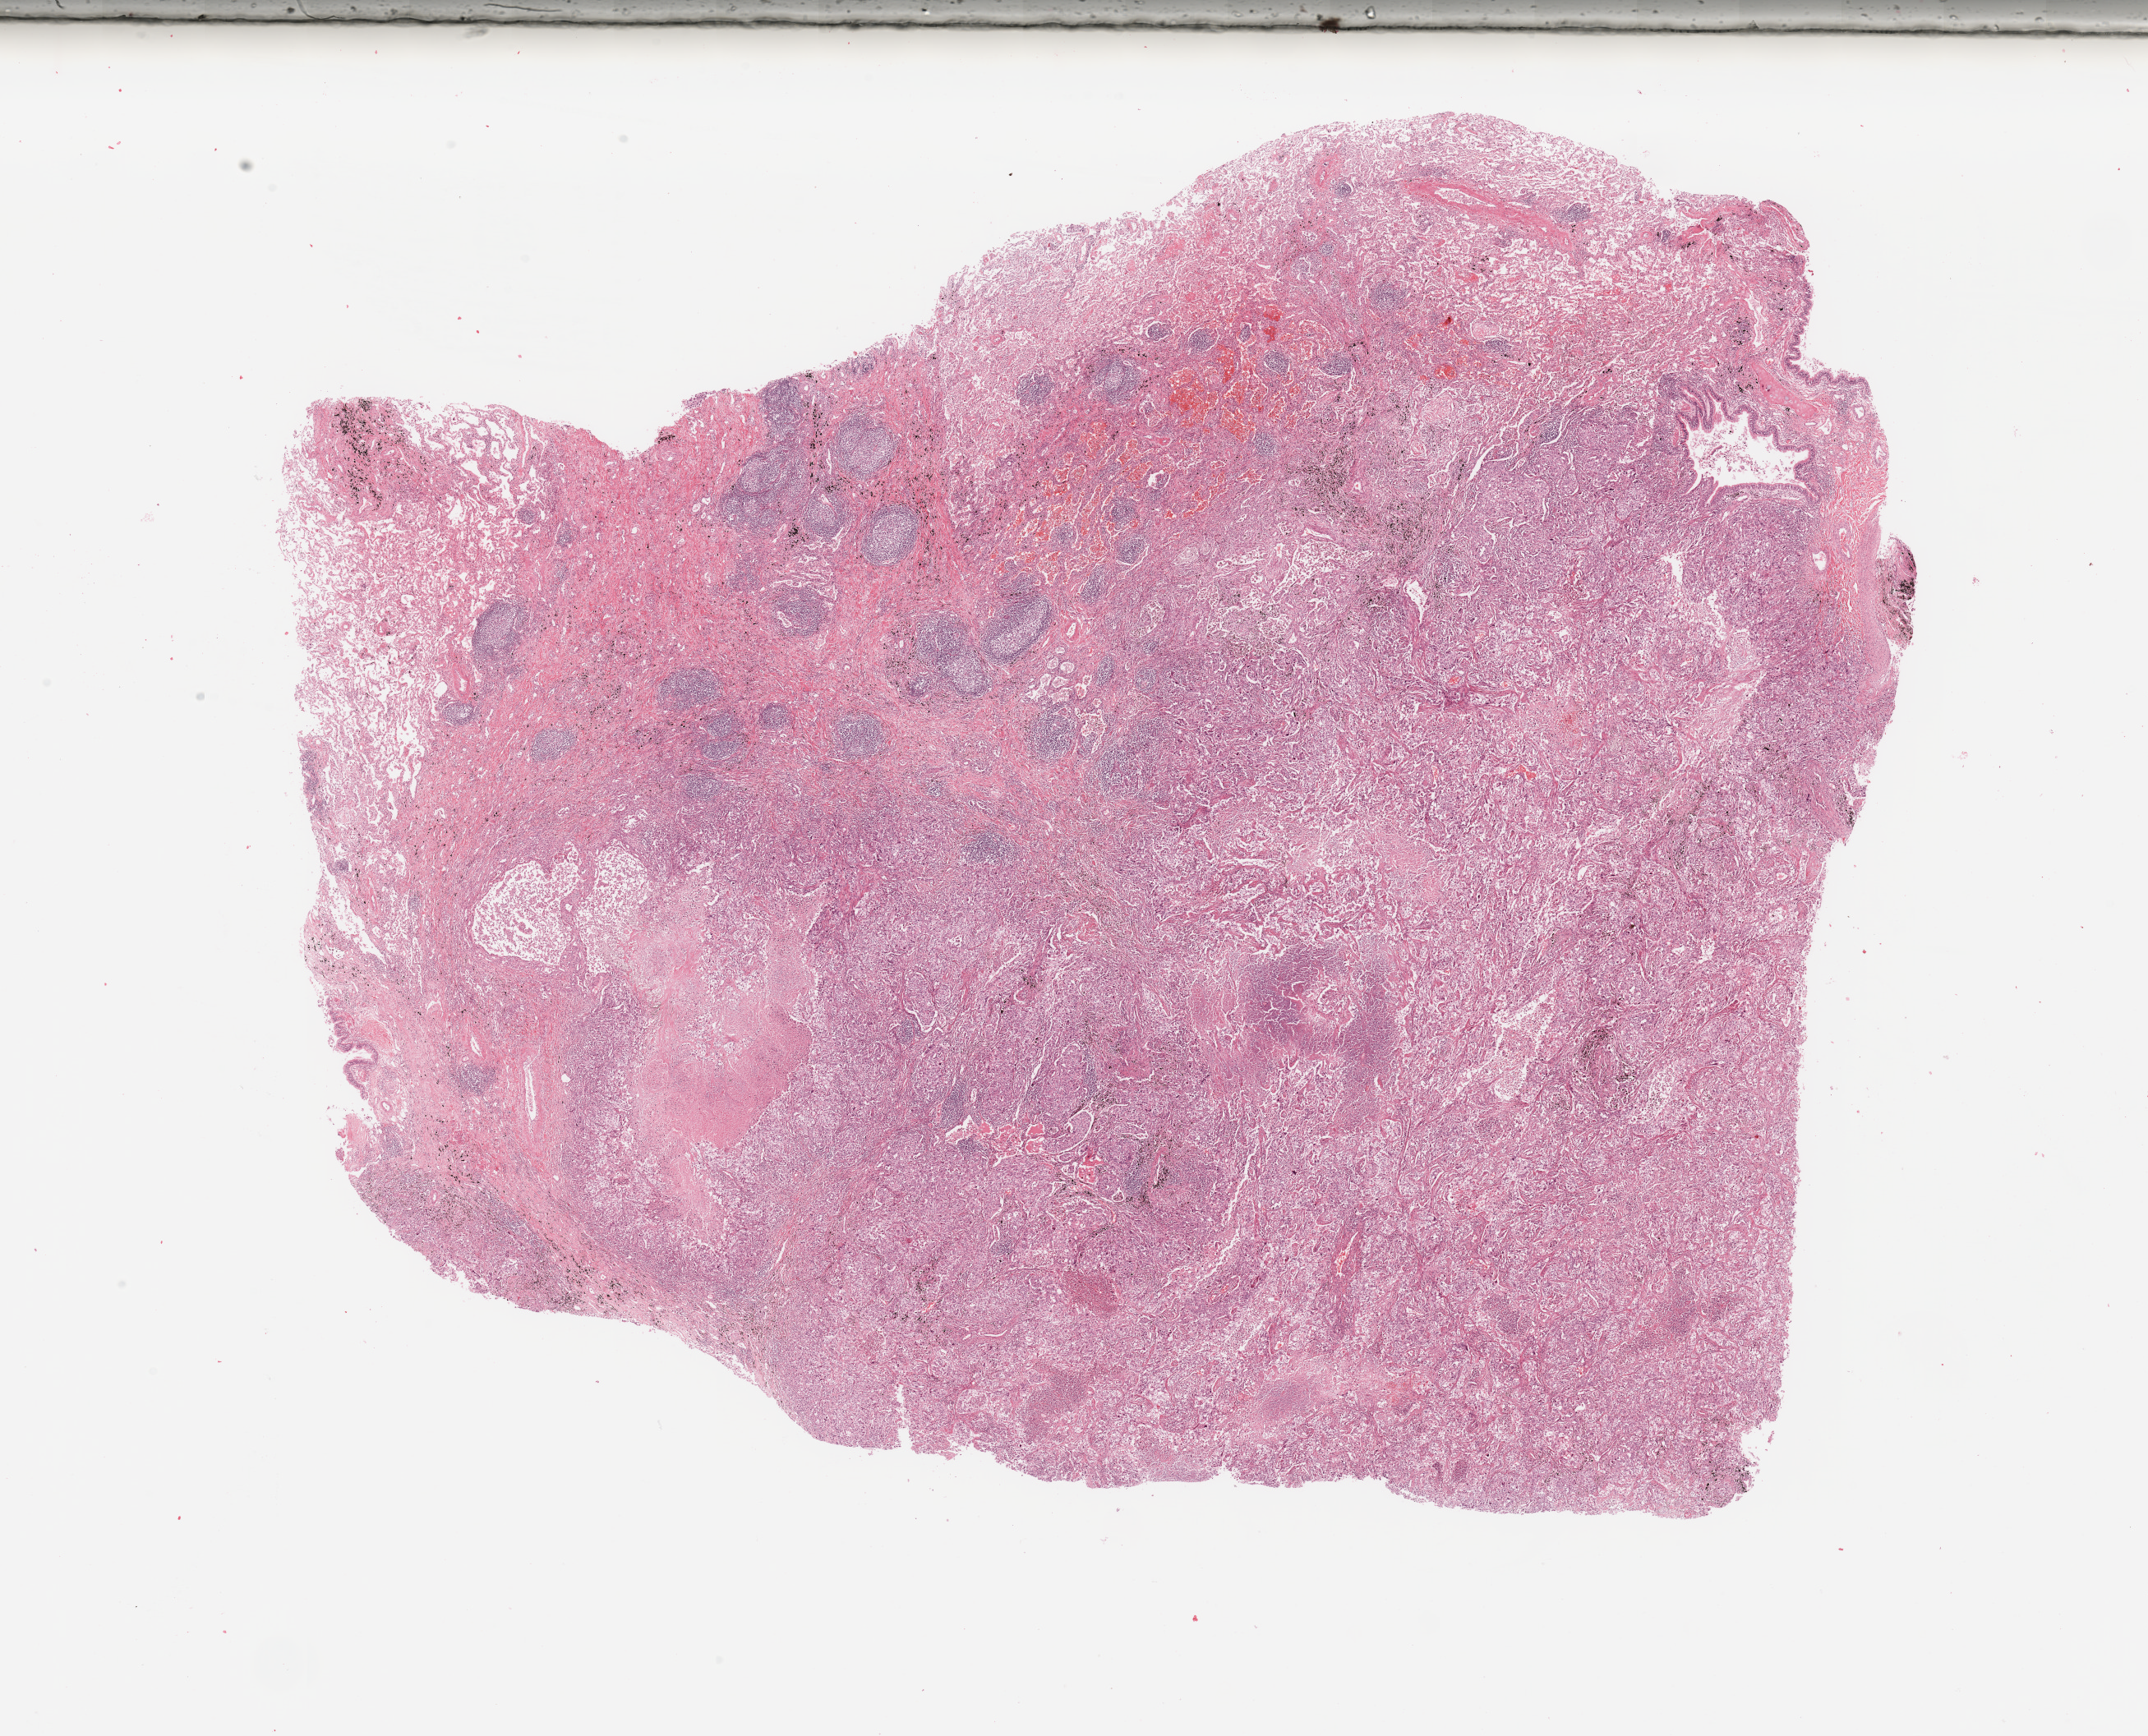
Whole-slide histology image, Hematoxylin and eosin (H&E) stained — whole scanned area (about 20.7 x 16.7 mm) shown as a low-resolution overview, tumour tissue sample, lung. Patient: male, age 69 years. Histologic grade: G3 (poorly differentiated).
AJCC pathologic stage: IIB. Histologic diagnosis: Adenocarcinoma, NOS.